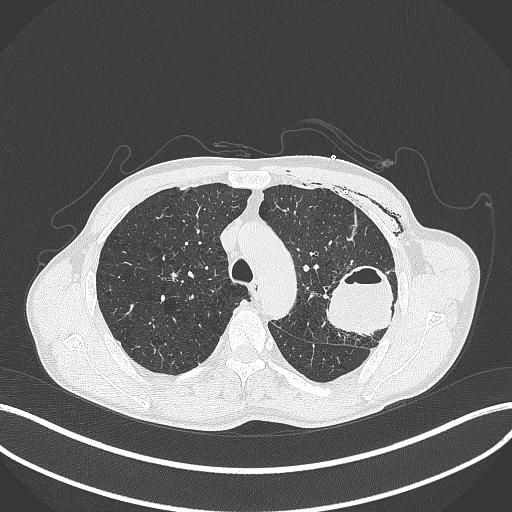
Chest CT, one axial slice. Position 296 of 457 along the scan axis. Reconstruction kernel B70f. 120 kVp. Lung window (W 1500 / L -600 HU). 1 mm slice thickness. 512 × 512 image matrix, field of view 400 × 400 mm. Male patient, age 58 years. Case-level facts recorded for this patient, not image findings: clinical TNM (as recorded): T3 N0 M0.
Outlined on this slice (bounding box drawn by a radiologist):
- lung tumour (recorded histology: adenocarcinoma): box from (x=321, y=261) to (x=397, y=338) px